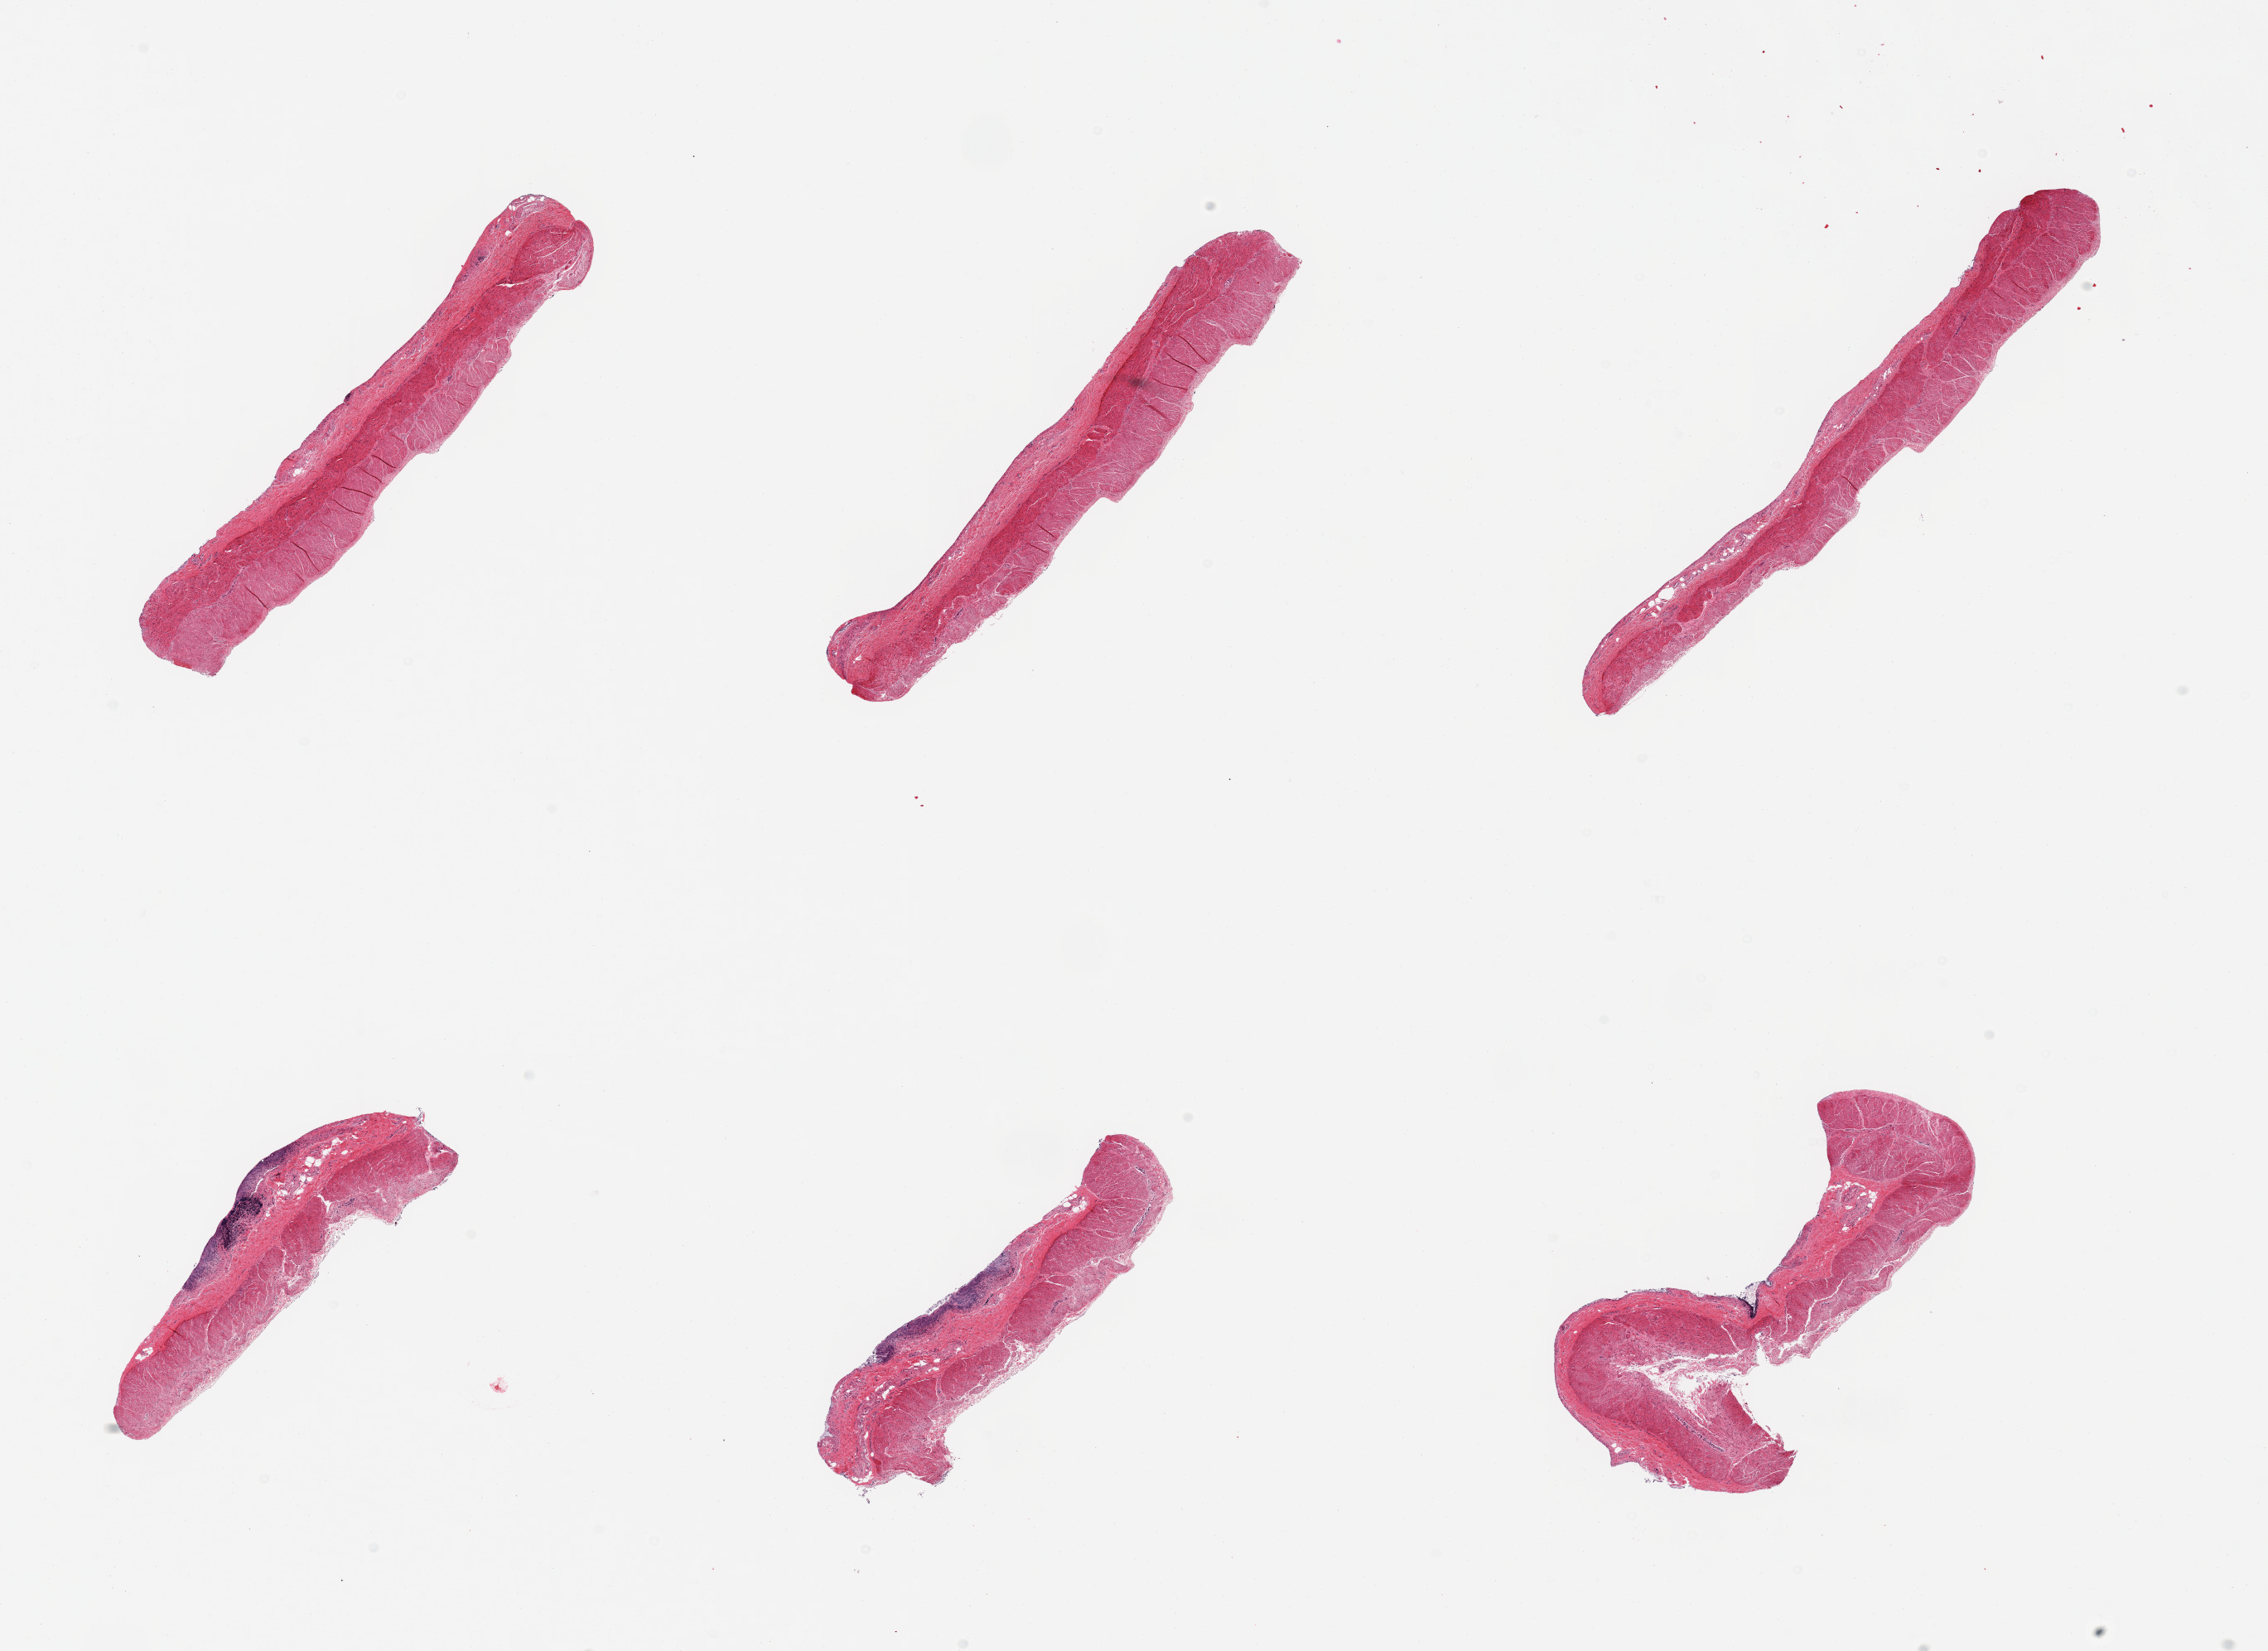
Whole-slide image, hematoxylin and eosin (H&E) stain — low-resolution overview of the scanned area, about 21.7 x 15.8 mm (acquisition: 20x scan). PAXgene-fixed paraffin-embedded (PFPE) section. Section of sigmoid colon (target tissue). Tissue donor sample.
- pathologist's review note for this sample: 6 pieces; predominantly muscularis, few pieces include residual autolyzed mucosa